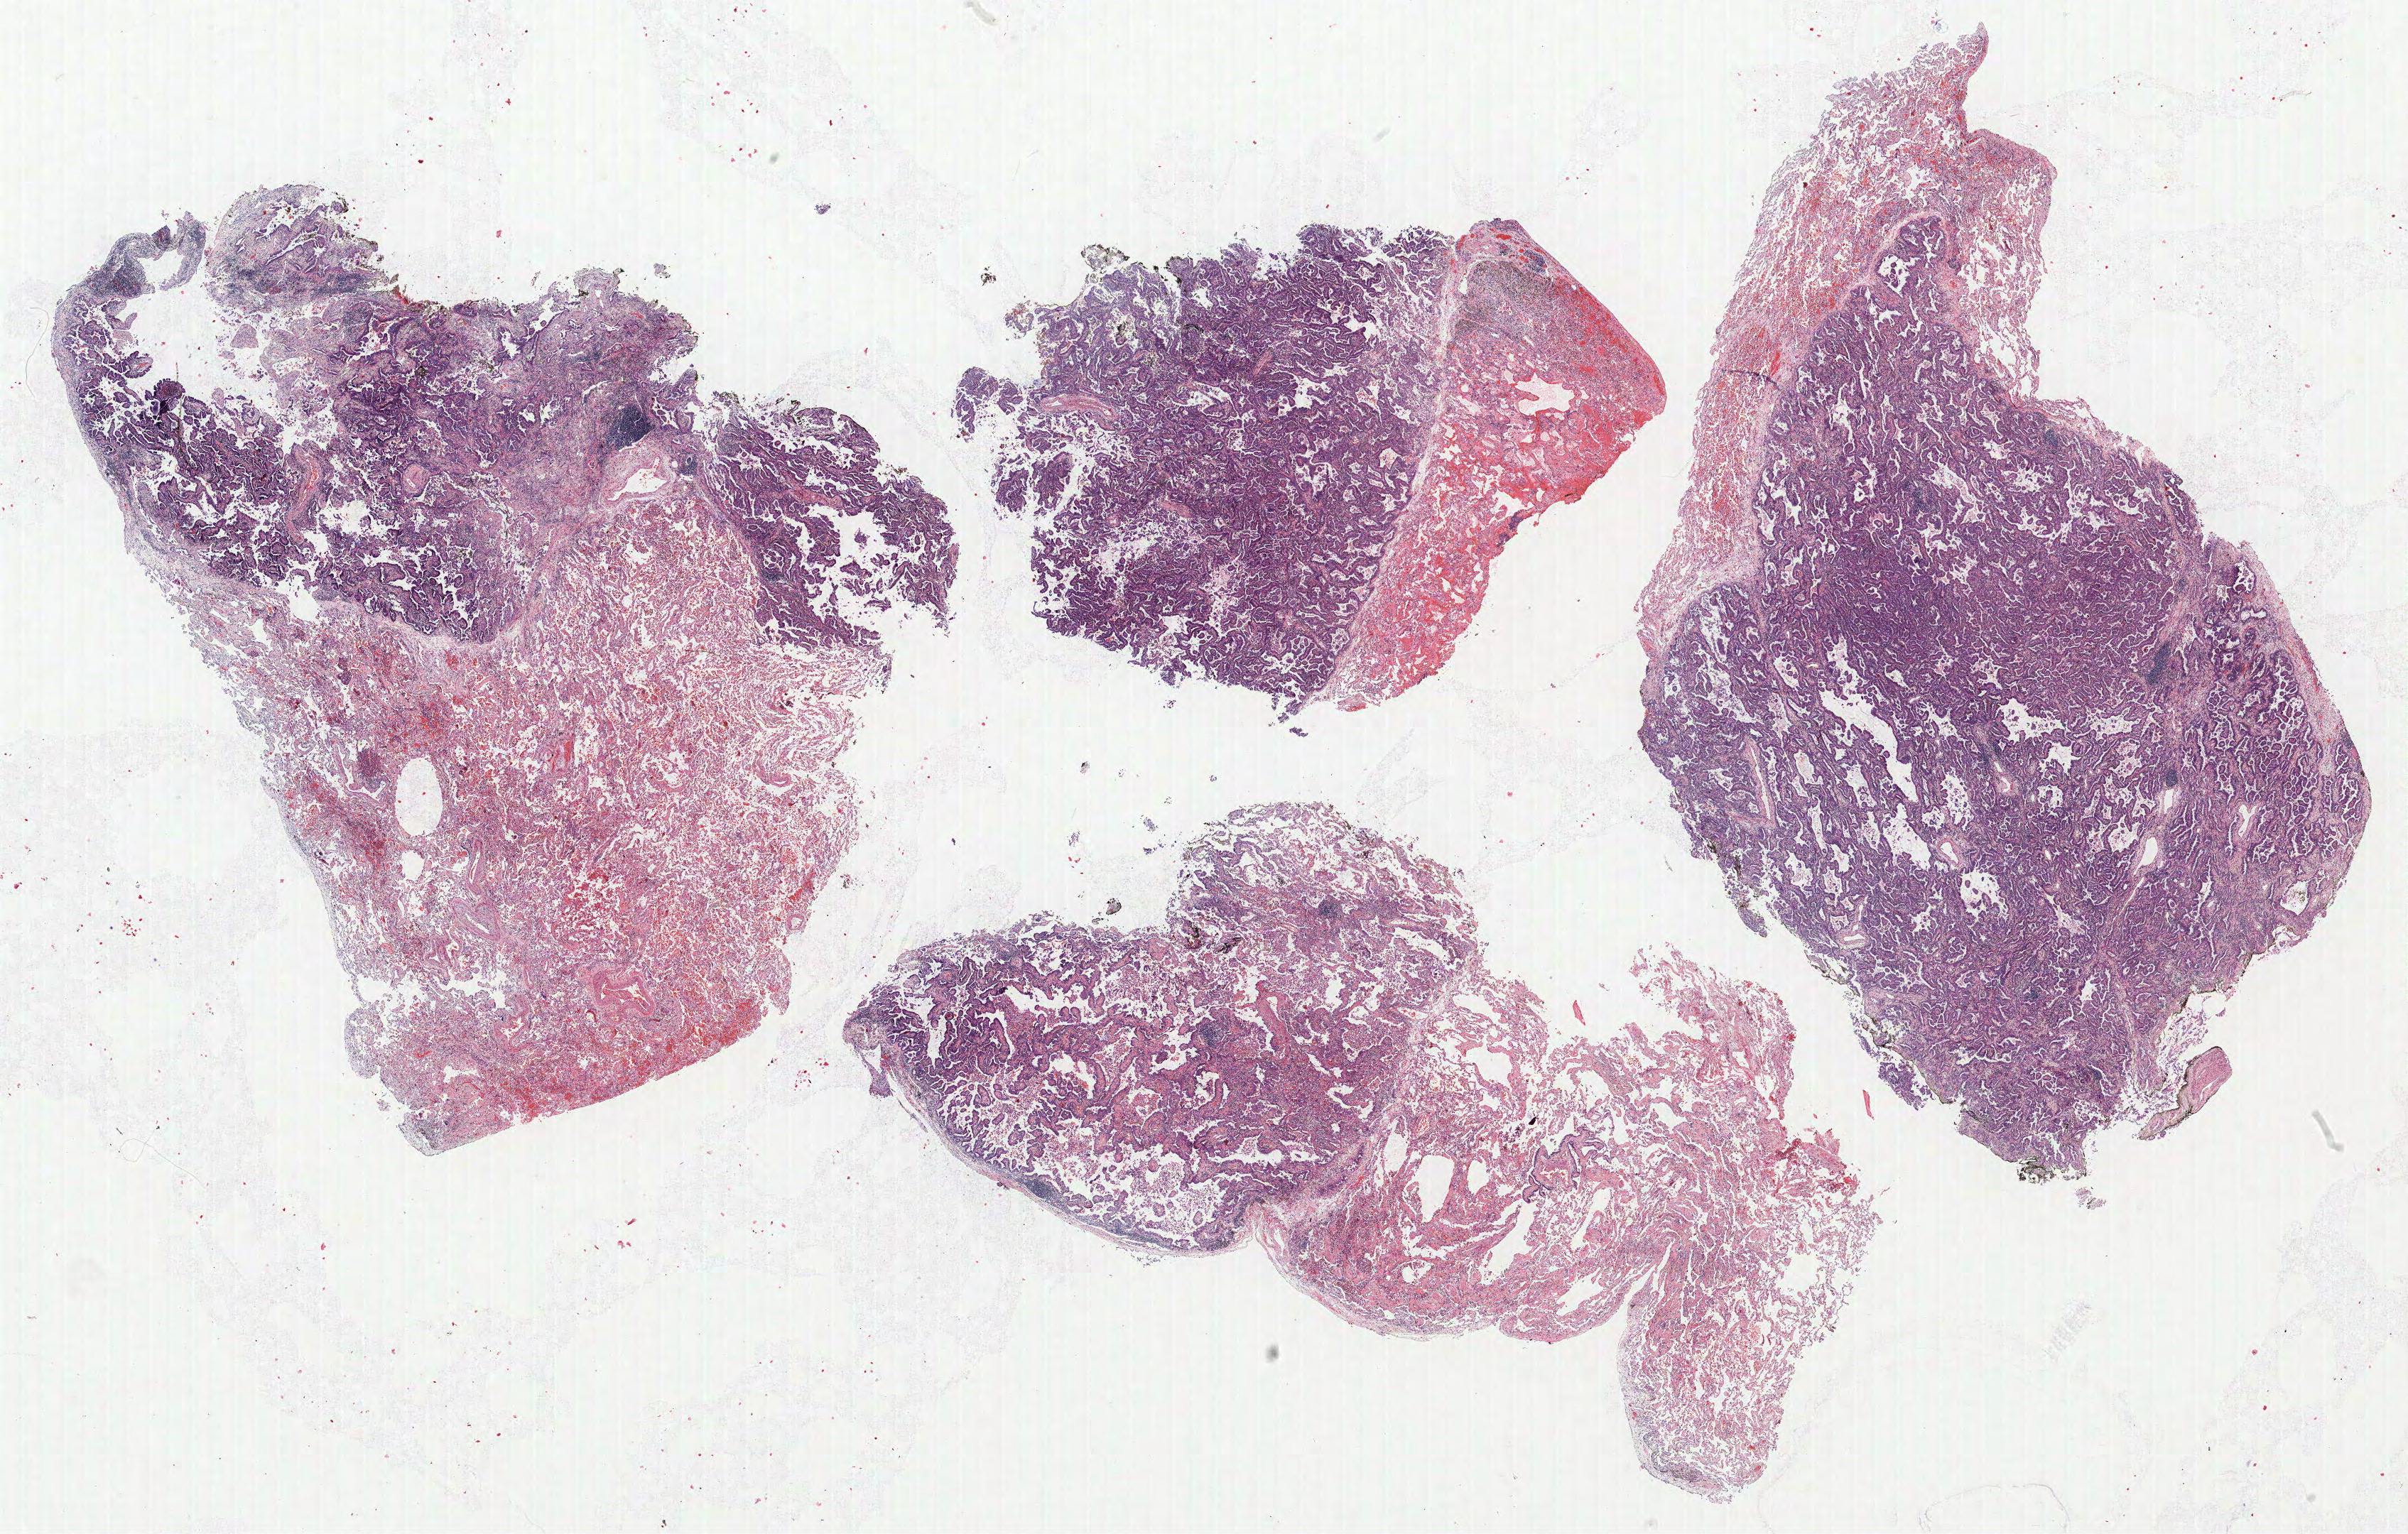
Hematoxylin and eosin (H&E) stained whole-slide image — low-resolution overview of the scanned area, about 27.1 x 17.3 mm (acquisition: 40x scan); FFPE section; lung. Male, age 60 at enrolment. Current smoker at enrolment. Grade: moderately differentiated (G2).
• participant's lung-cancer diagnosis: Papillary adenocarcinoma, NOS (ICD-O-3 8260/3)
• stage (AJCC 6th edition): IB
• tumour size (pathology): 35 mm
• primary tumour location (clinical record): left lower lobe